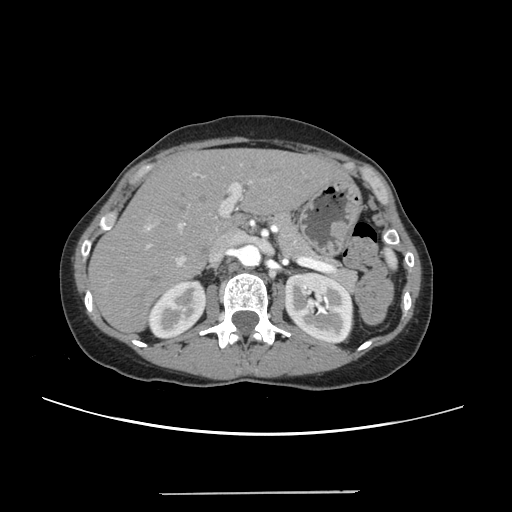
Contrast-enhanced abdominal CT, one axial slice; slice 151 of 240 in the series (ordered by position); intravenous contrast given; soft-tissue window (W 400 / L 40 HU); 512 × 512 image matrix. Female patient, age 60 years. Case-level facts recorded for this patient, not image findings: diagnosis: colorectal cancer liver metastases, imaged before liver resection; multiple liver metastases: no; largest metastasis: 1.5 cm.
Structures marked on this image (expert manual segmentation):
- liver: box from (x=91, y=150) to (x=344, y=330) px
- planned liver remnant (the part of the liver to remain after resection): (x=91, y=150)–(x=343, y=330)
- portal vein (with intrahepatic branches): (x=143, y=171)–(x=254, y=266)